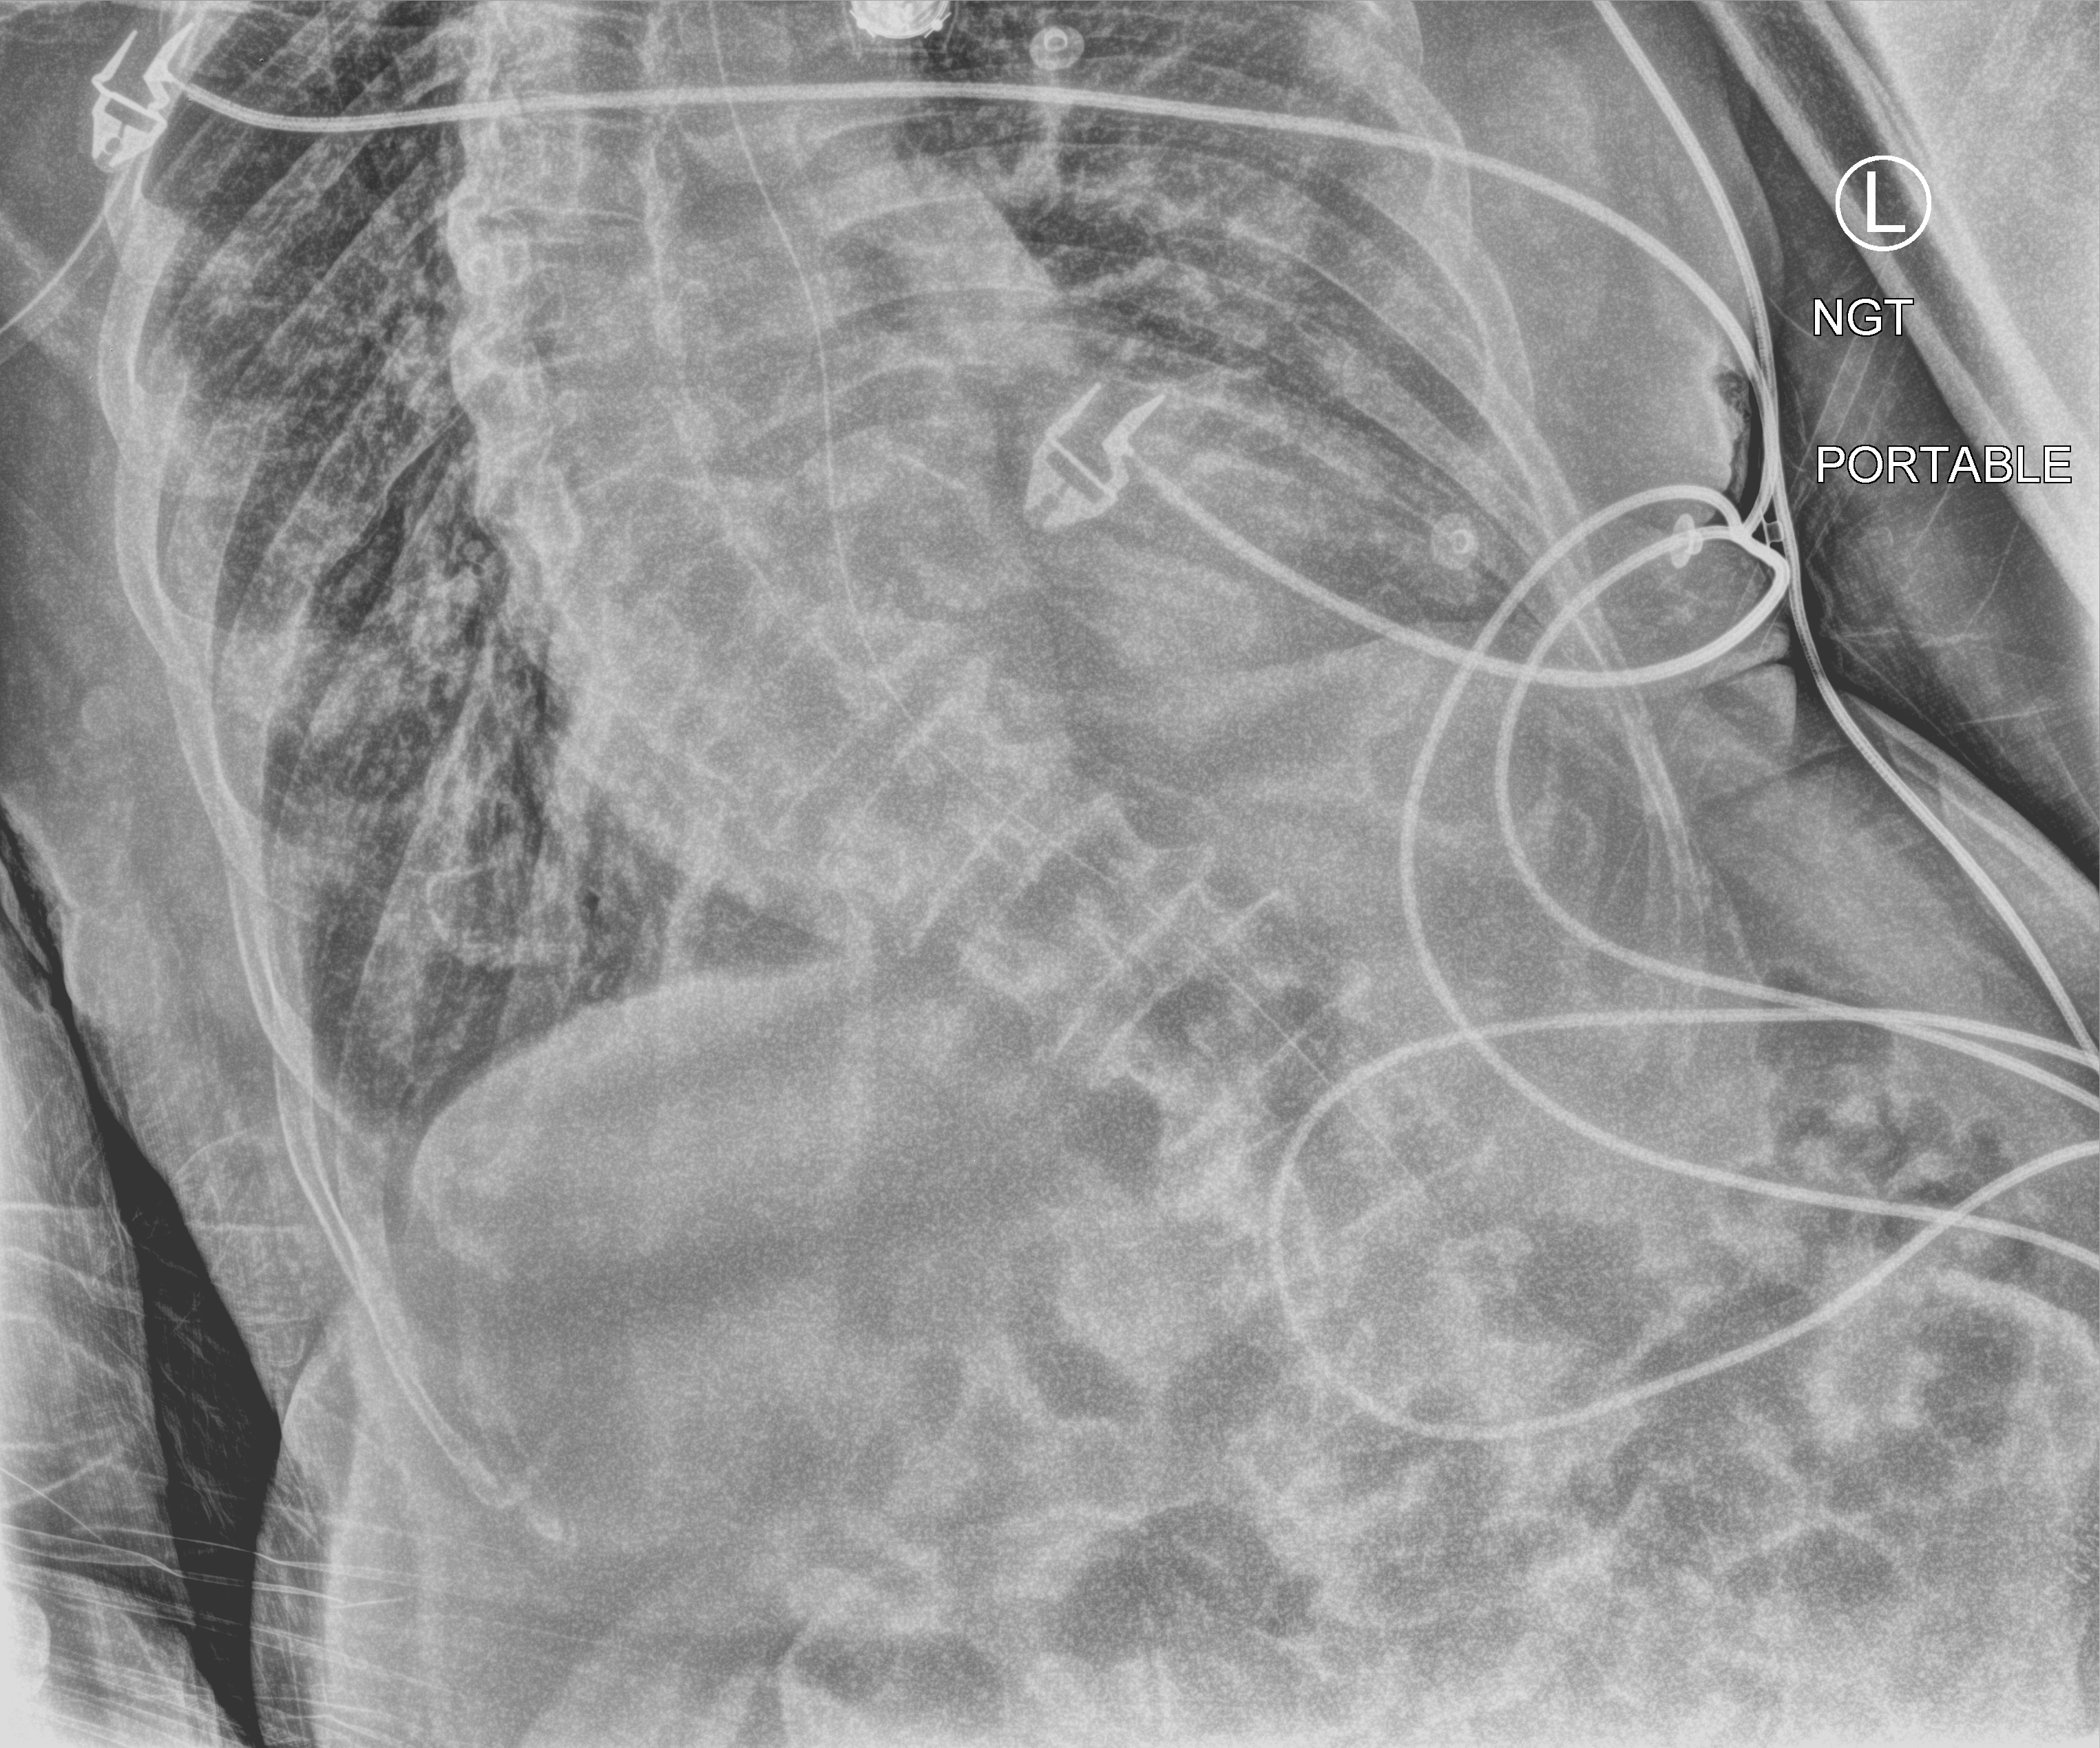
Chest X-ray (portable), anteroposterior (AP) projection. Patient hospitalised with COVID-19; male, aged 75–90 years.
Admission-level facts for this patient (not findings on this image; timing relative to this image not recorded): length of hospital stay: 12 days.